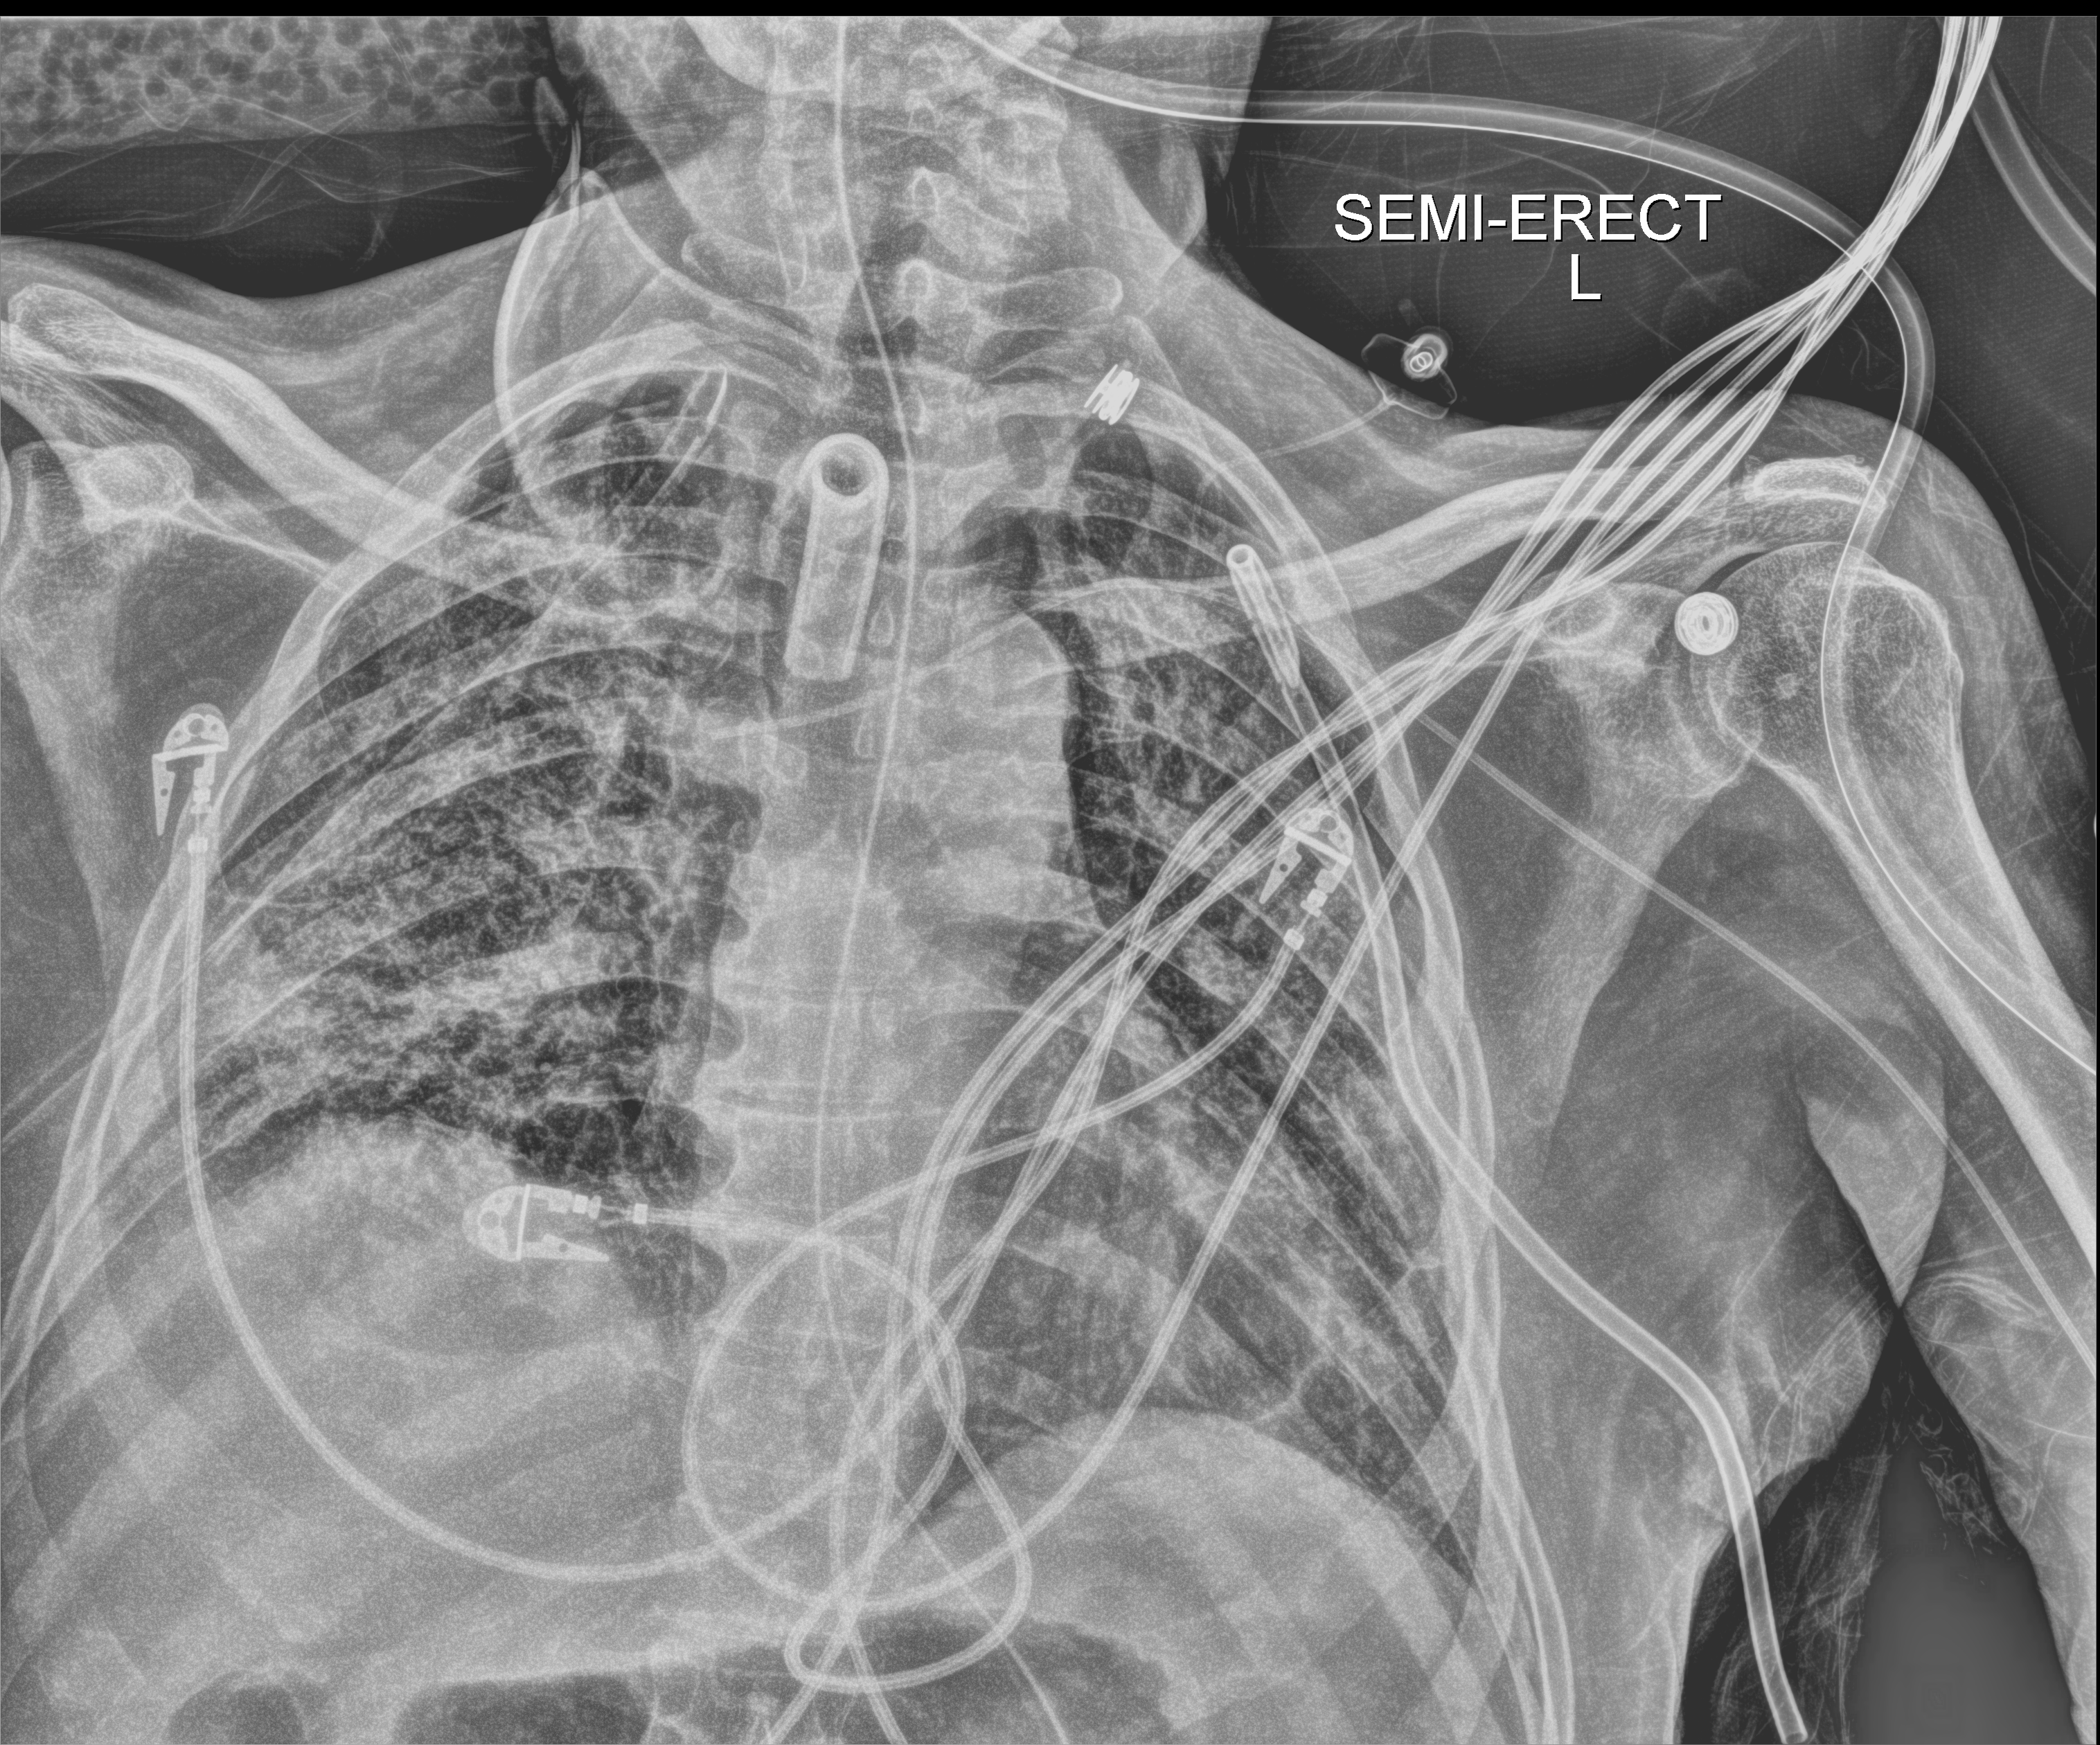
Bedside chest radiograph (digital radiography). Male patient hospitalised with COVID-19, age 18–59 years.
From the hospital-stay record, not from the radiograph (when in the stay this image was taken is not recorded):
- COPD (admission record): no
- length of hospital stay: 83 days
- mechanically ventilated during this hospital stay: yes